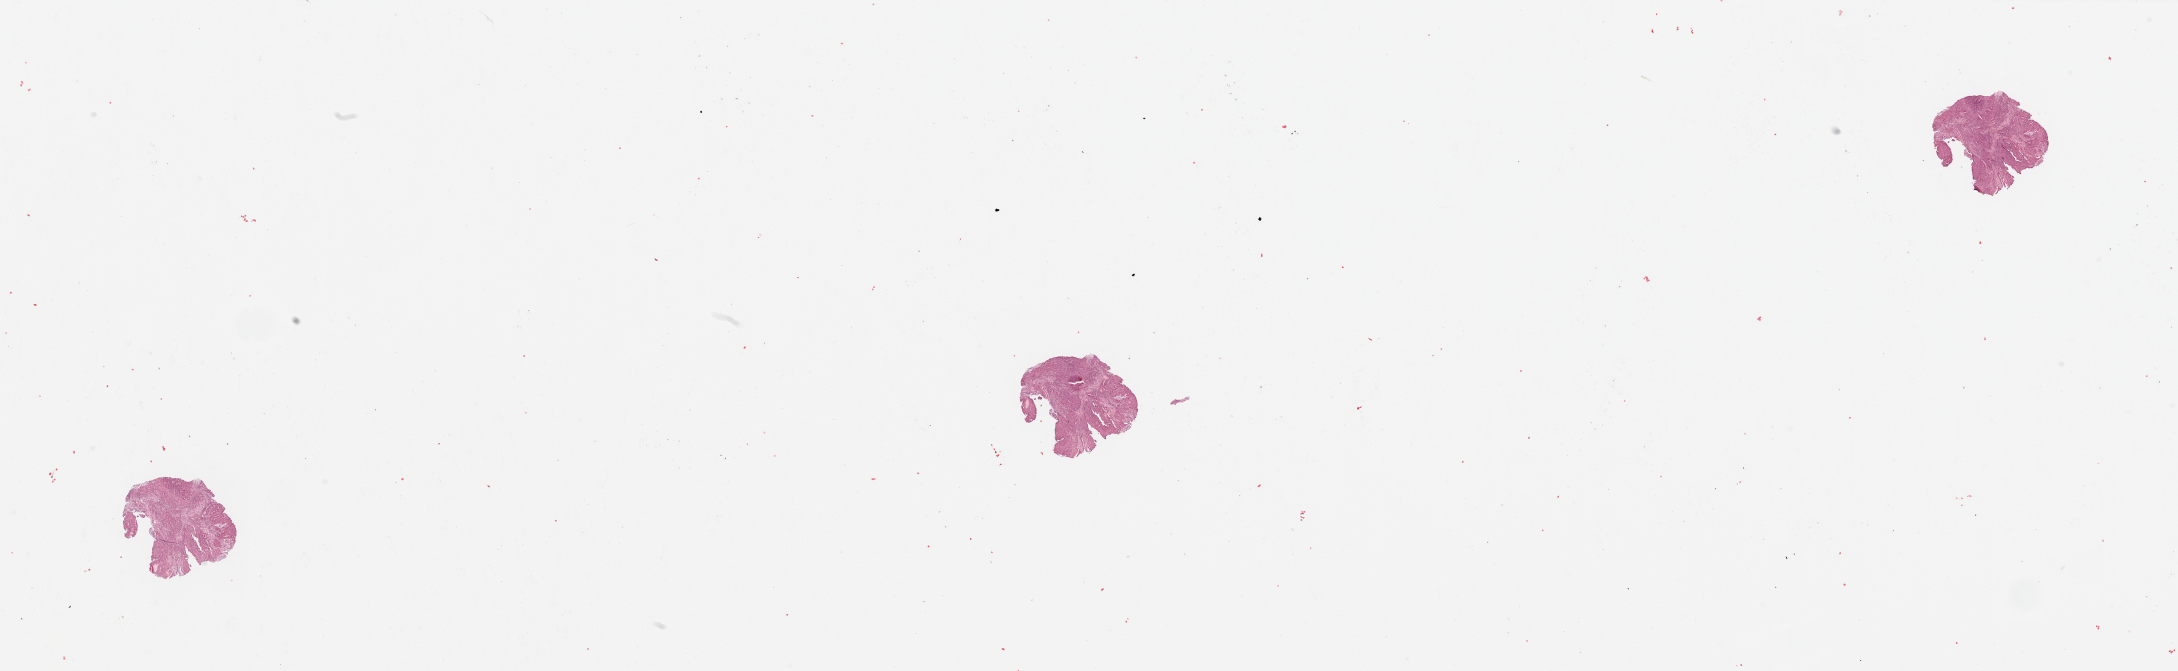
Whole-slide histology image, H&E — shown as a low-resolution overview of the whole scanned area (about 34.5 x 10.6 mm, acquisition: 20x scan). Tumour tissue sample, sampled site: larynx. 62-year-old male patient. Histologic grade: G3 (poorly differentiated). Slide review estimates, as recorded: tumour nuclei 85%, necrosis 0%.
- diagnosis: Squamous cell carcinoma, NOS (larynx, NOS)
- AJCC pathologic stage: IVA